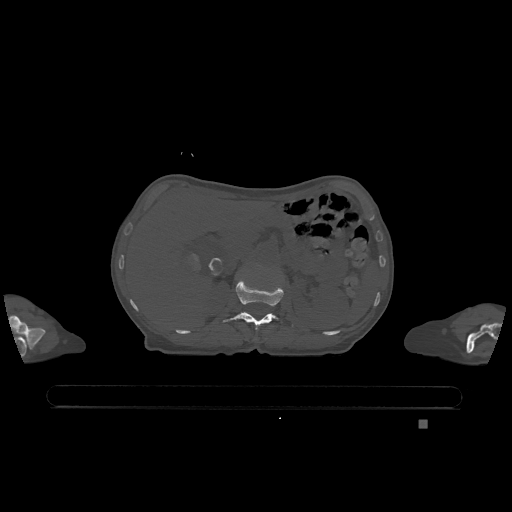
CT including the spine, one axial slice; position 469 of 1317 along the scan axis; bone window (W 1800 / L 400 HU); 0.5 mm slice thickness; 512 × 512 image matrix, field of view 500 × 500 mm. Patient: female, 74 years. Case-level facts recorded for this patient, not image findings: primary cancer: lung; vertebrae with lytic lesions (as recorded): T1, T4, T5, T6, L4, L5.
Annotated regions visible in this slice (semi-automatic segmentation, software-assisted and operator-edited):
- L1 vertebra: bounding box [x1, y1, x2, y2] px = [223, 279, 294, 329]